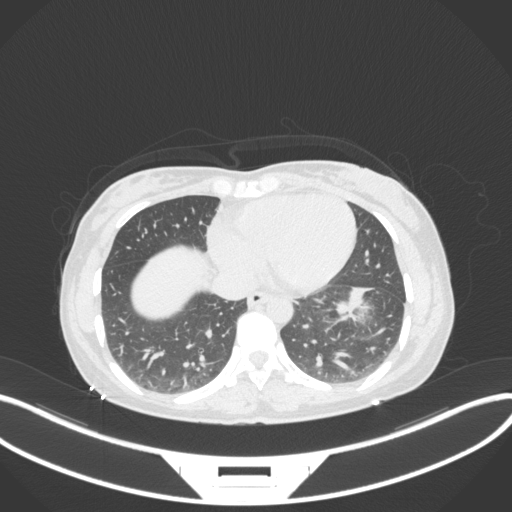
Chest CT, one axial slice. Slice 118 of 361 in the series (ordered by position). 120 kVp. Lung window (W 1500 / L -600 HU). 1 mm slice thickness. 512 × 512 image matrix. Female patient, age 41 years. Case-level facts recorded for this patient, not image findings: clinical TNM (as recorded): T2a N3 M1b.
Outlined on this slice (rectangle marked by the reading radiologist):
- lung tumour (recorded histology: adenocarcinoma): box from (x=335, y=282) to (x=379, y=321) px